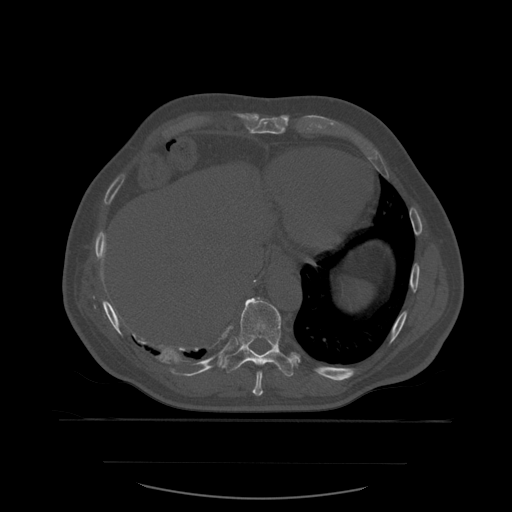
CT including the spine, one axial slice. Position 322 of 590 along the scan axis. Bone window (W 1800 / L 400 HU). 1.25 mm slice thickness. 512 × 512 image matrix, field of view 479 × 479 mm. Patient age 71 years. Case-level facts recorded for this patient, not image findings: primary cancer: lung.
Outlined on this slice (semi-automatically segmented with operator editing):
- T10 vertebra: bounding box [x1, y1, x2, y2] px = [226, 297, 298, 377]
- T9 vertebra: [253, 371, 264, 396]